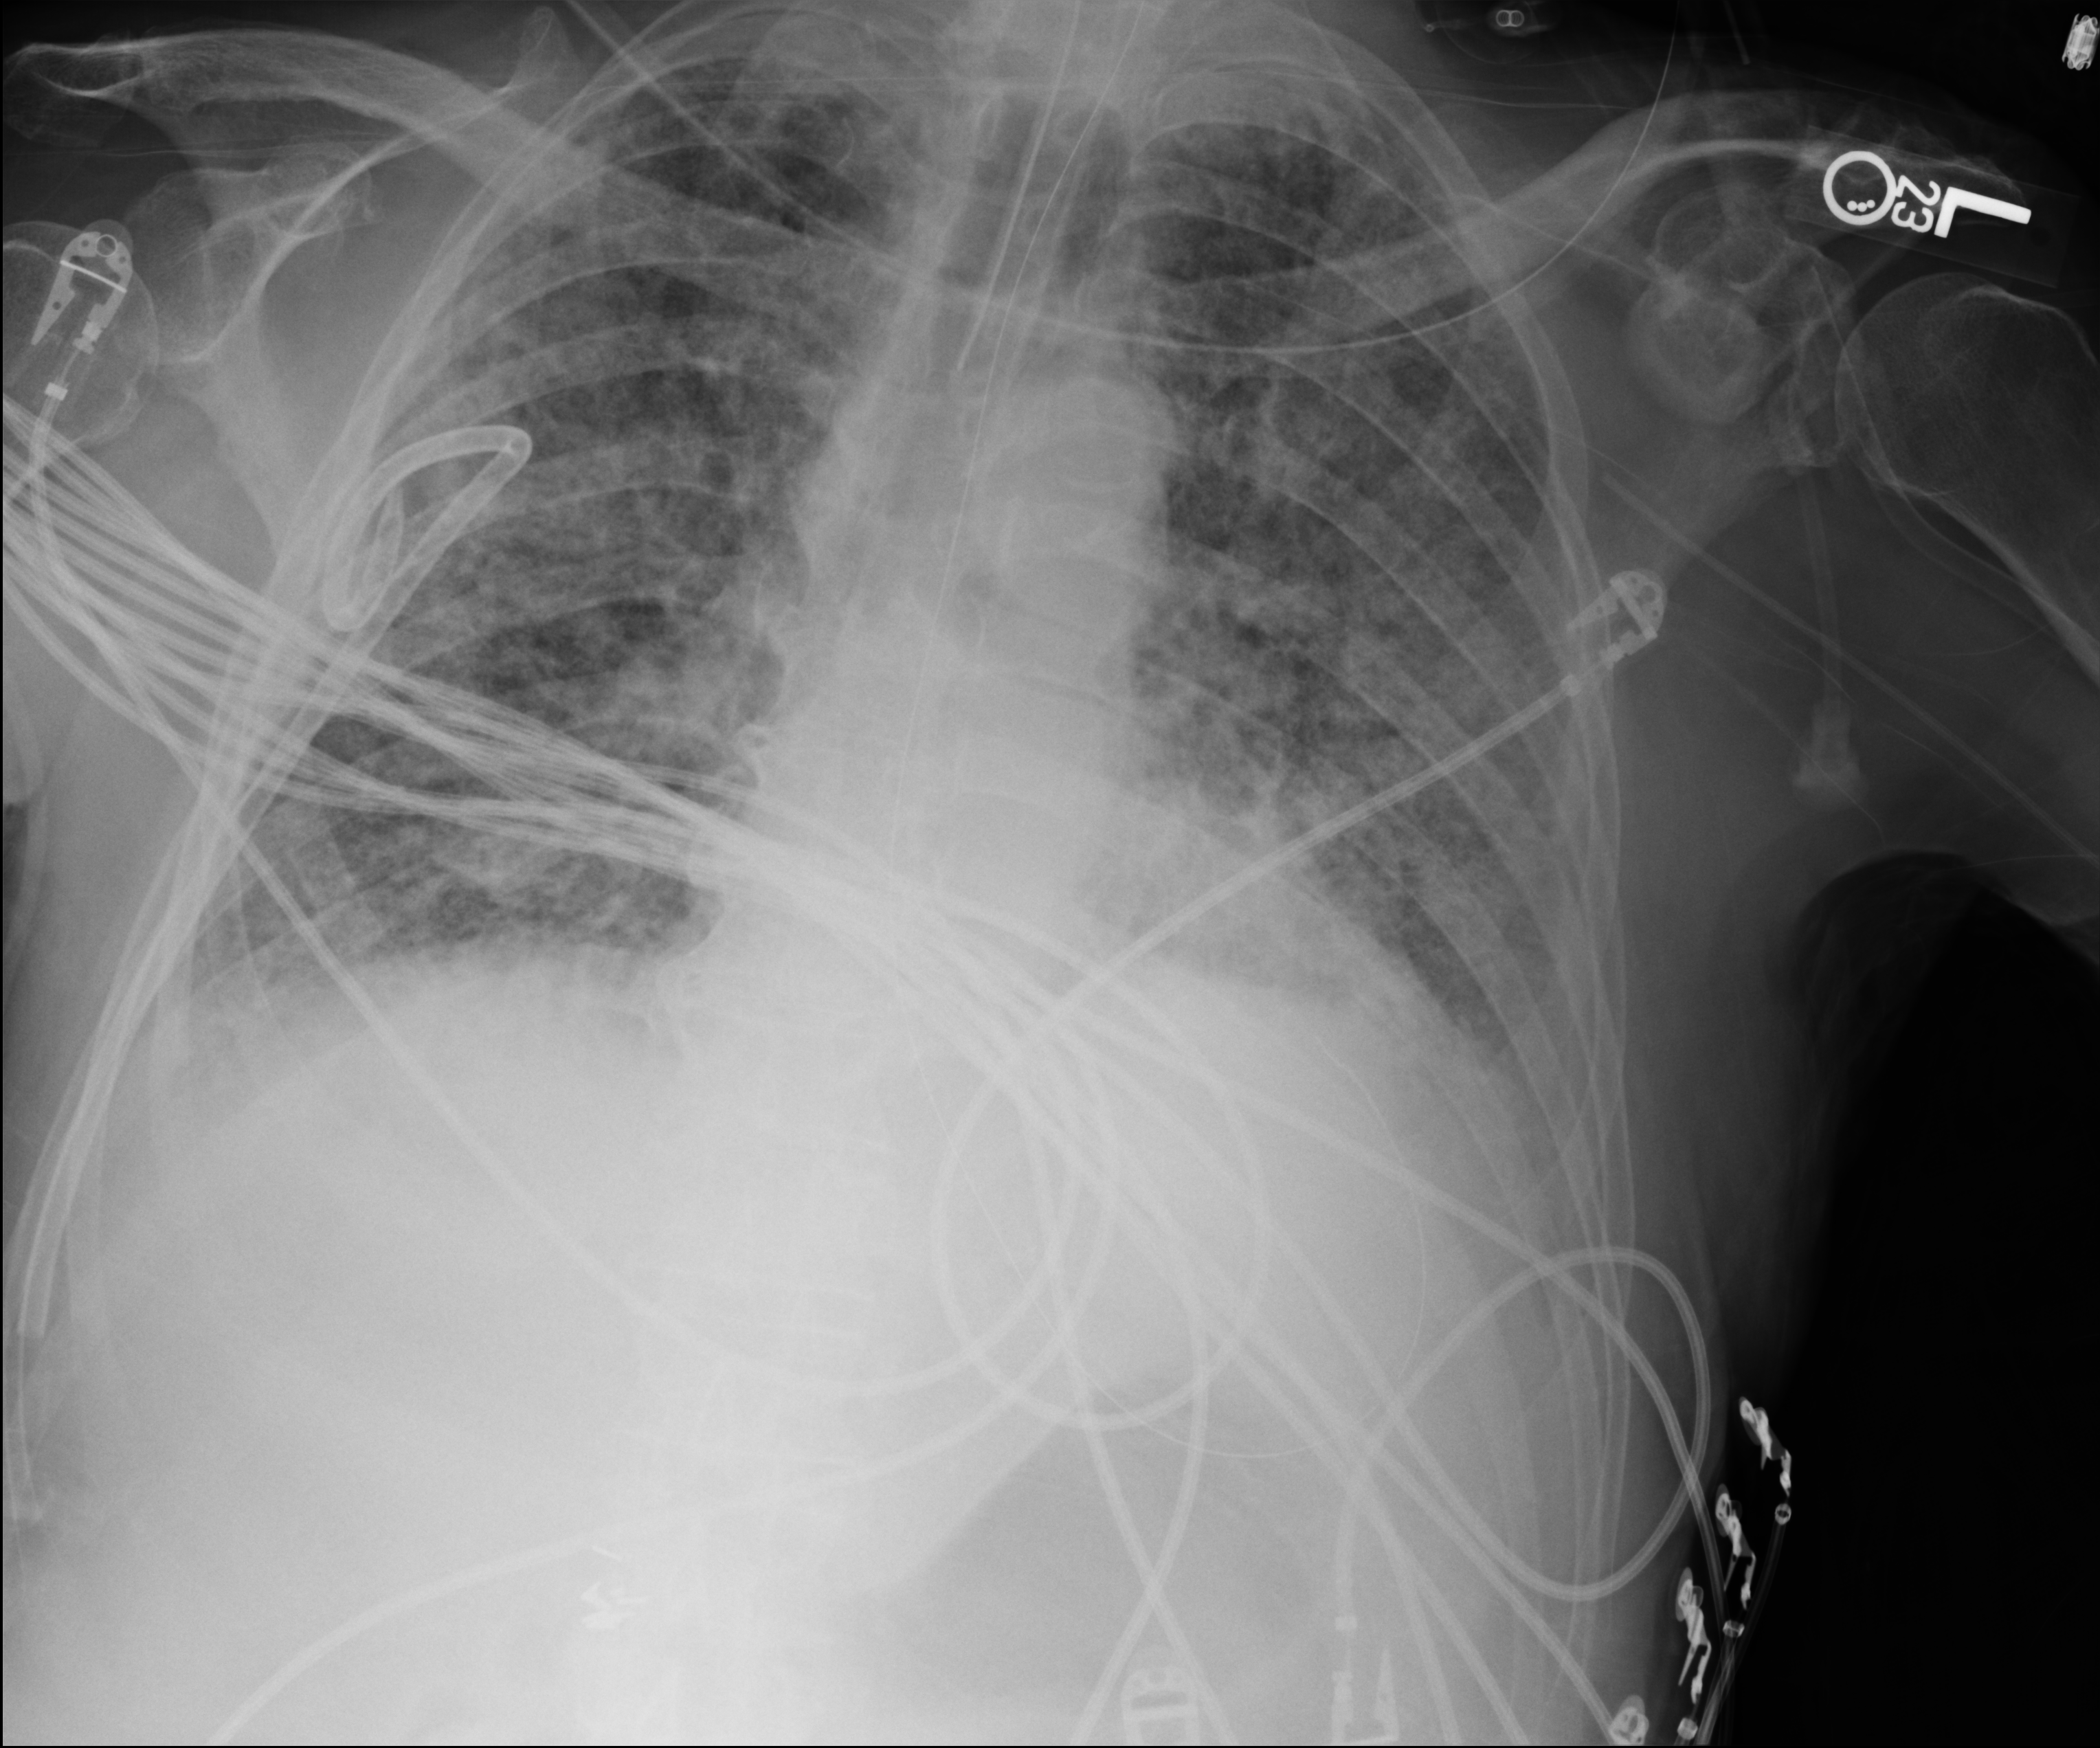
Bedside chest radiograph (computed radiography); anteroposterior (AP) projection. Male patient hospitalised with COVID-19, age 75–90 years.
Admission-level facts for this patient (not findings on this image; timing relative to this image not recorded):
- mechanically ventilated during this hospital stay: yes